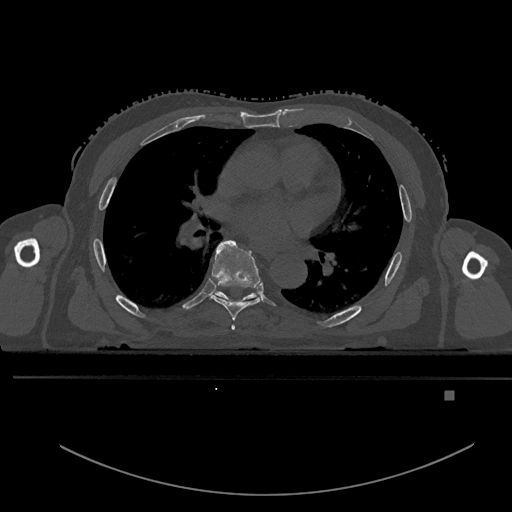
CT including the spine, one axial slice. Position 291 of 969 along the scan axis. Bone window (W 1800 / L 400 HU). 0.5 mm slice thickness. 512 × 512 image matrix. Male patient, age 82 years. From the clinical record (not read from this slice): primary cancer: prostate; vertebrae with lytic lesions (as recorded): T11, T9, T8, T2.
Annotated regions visible in this slice (semi-automatic segmentation, software-assisted and operator-edited):
- T5 vertebra: bounding box (x1, y1, x2, y2) in pixels: (231, 325, 236, 331)
- T6 vertebra: (210, 240, 261, 321)
- T7 vertebra: (214, 291, 256, 300)